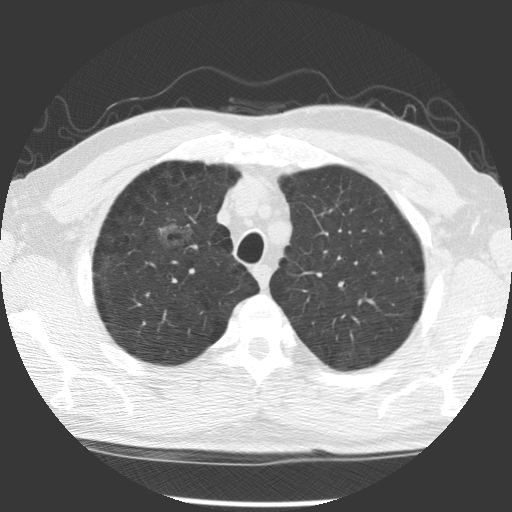
Axial slice from a low-dose chest CT screening exam, first (baseline) screen, lung window (W 1500 / L -600 HU), 2.5 mm slice thickness, standard (soft-tissue) reconstruction kernel (STANDARD), slice 93 of 122 in the series. Male participant, aged 60 years at enrolment. Former smoker at enrolment.
• Lesion marked by an expert reader, bounding box (x1, y1, x2, y2) in pixels: (142, 214, 200, 263).
• Screening reader's record for this exam (one nodule recorded; not confirmed to be the boxed lesion): non-calcified nodule or mass ≥4 mm, right middle lobe, 20 × 20 mm, poorly defined margins, ground glass attenuation.
• Official screen result: positive, change unspecified: nodule(s) >= 4 mm or enlarging nodule(s), mass(es), or other non-specific abnormalities suspicious for lung cancer.
• Later outcome: lung cancer diagnosed 863 days after this screen — papillary adenocarcinoma, NOS, right upper lobe, moderately differentiated (G2), stage IB (AJCC 6th edition), 32 mm at pathology.